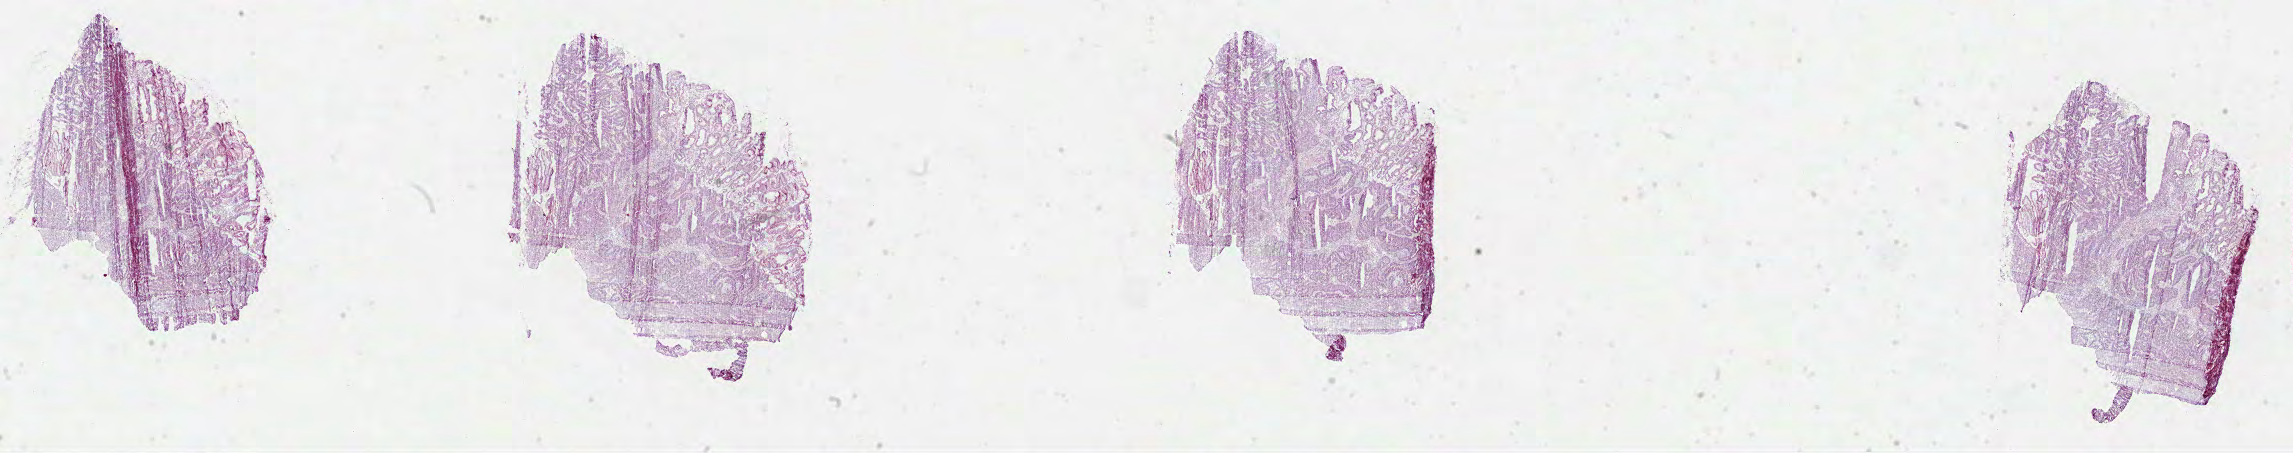
Hematoxylin and eosin (H&E) stained whole-slide image — a low-resolution overview of the entire scanned area, about 37.0 x 7.3 mm; FFPE section; primary tumour sample from the stomach. Patient: male, age at initial diagnosis 77 years.
Pathologic diagnosis: Tubular adenocarcinoma (body of stomach).